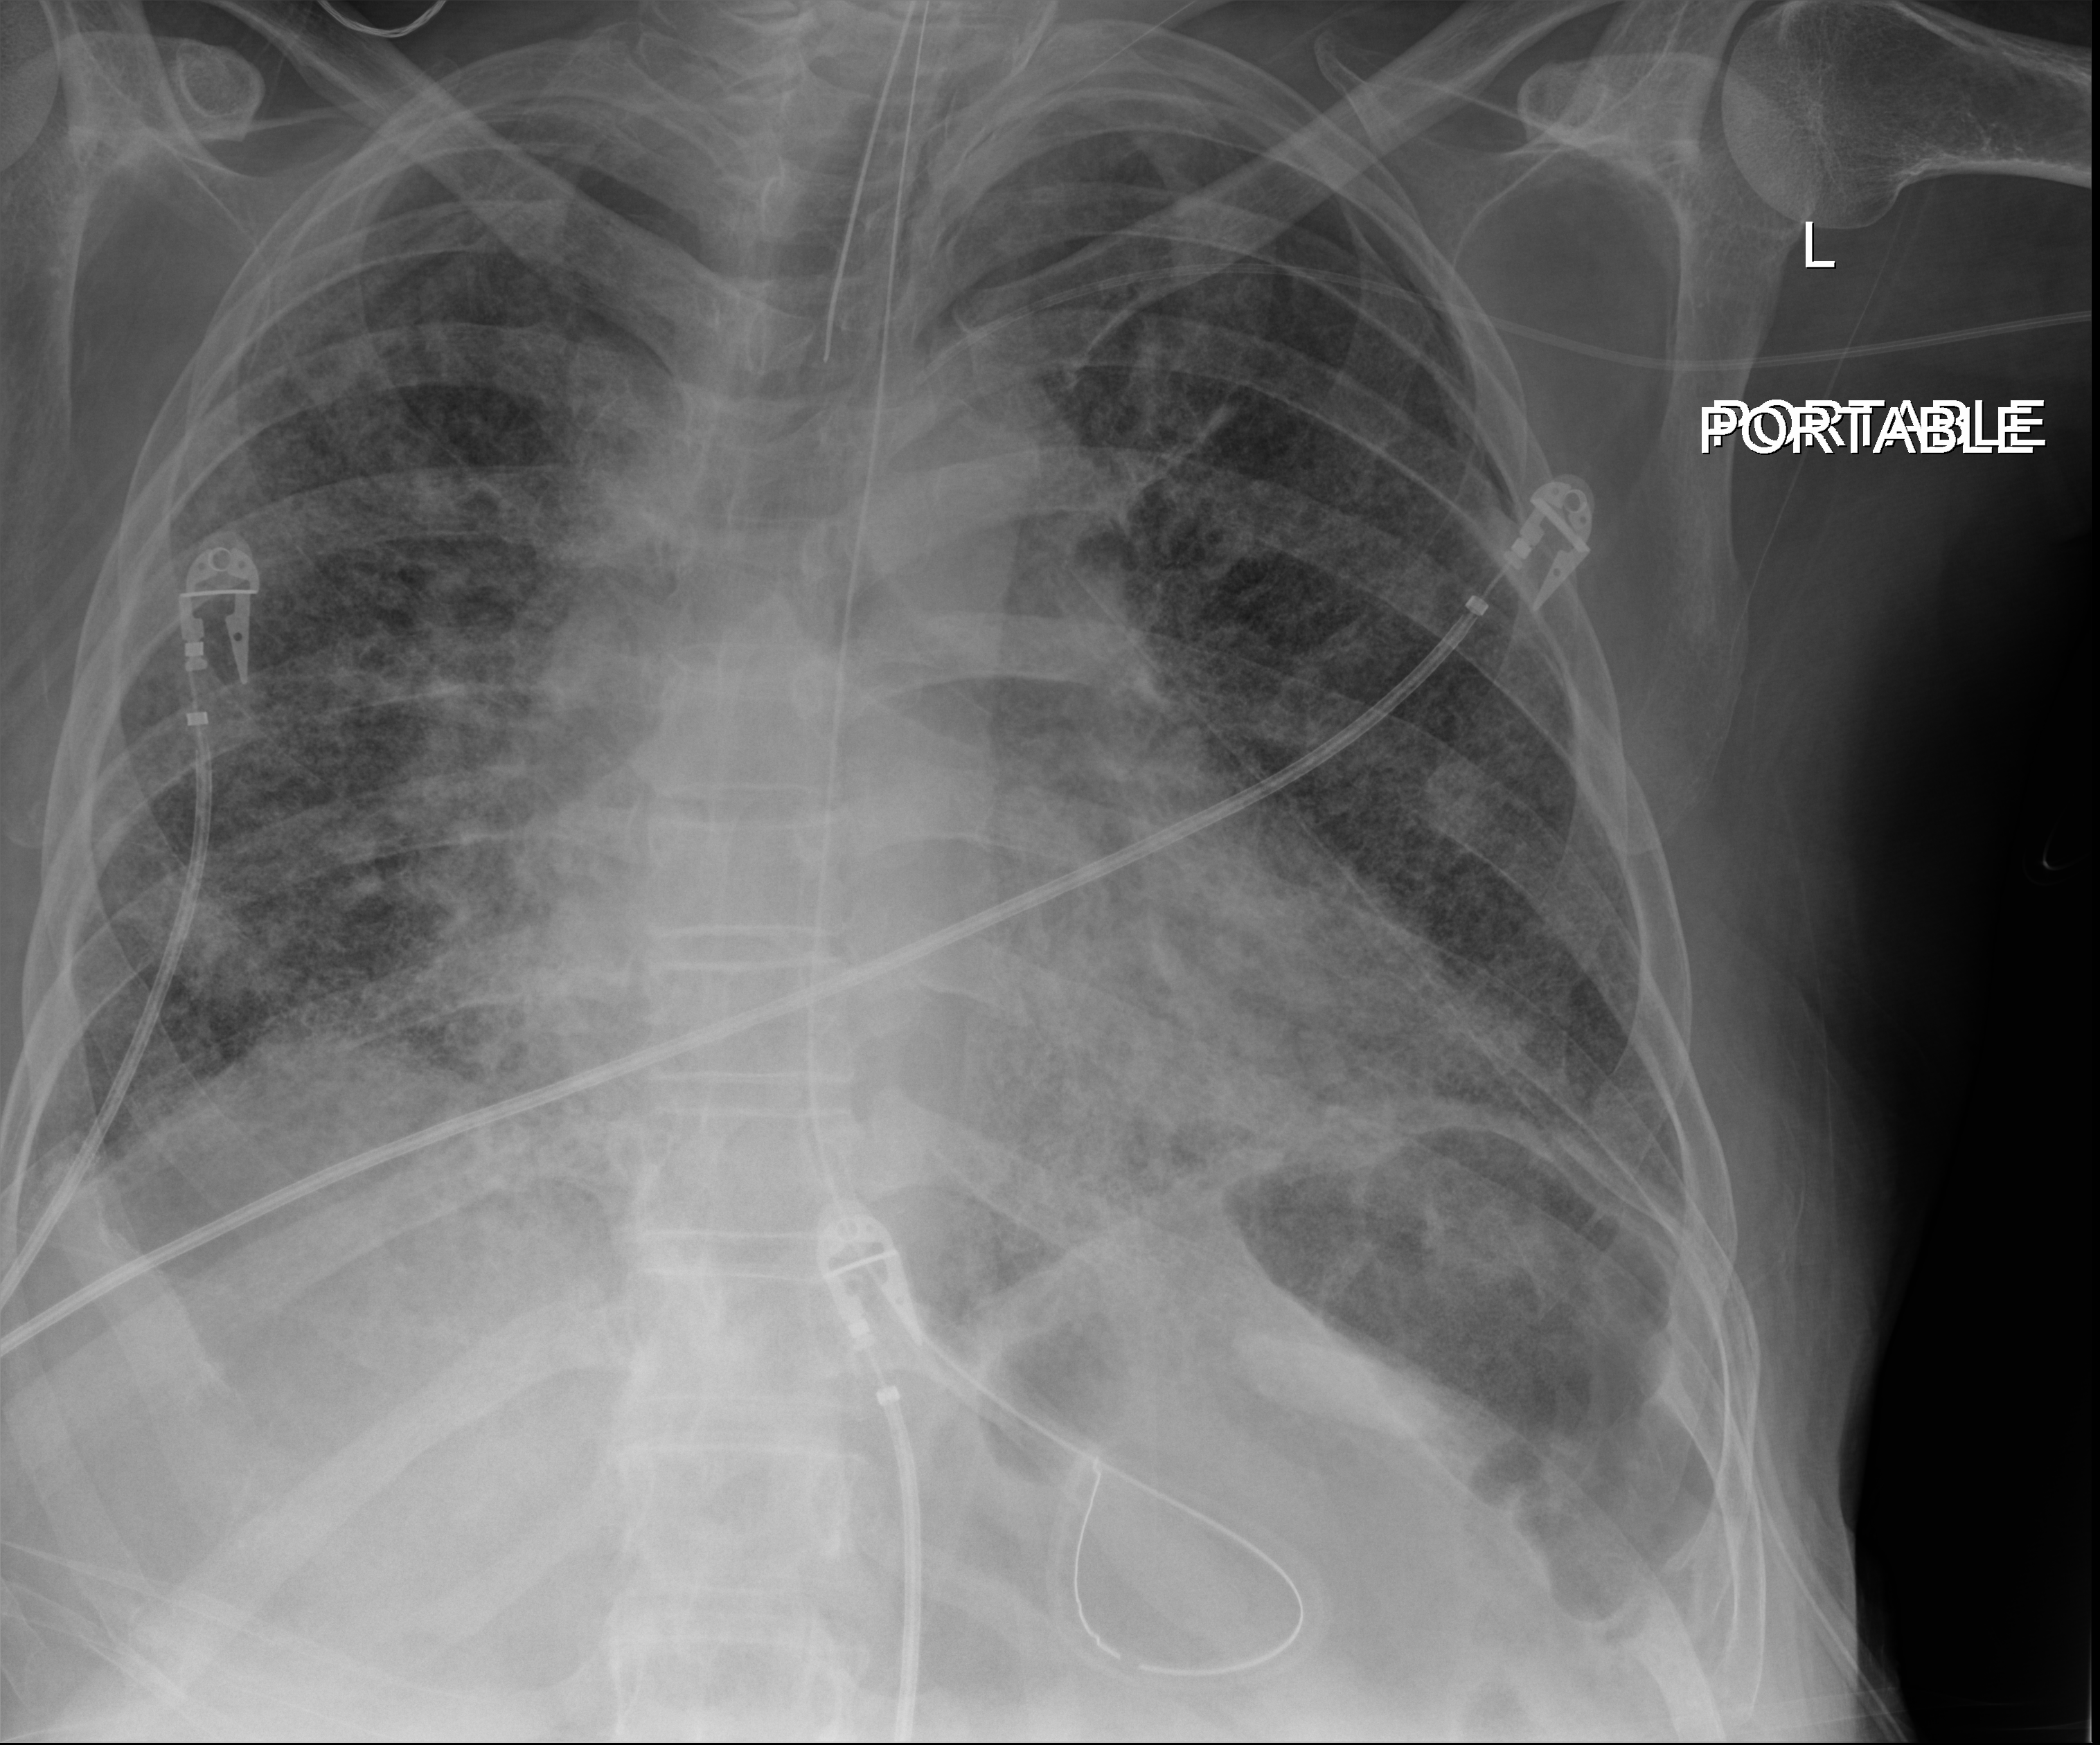
Portable chest radiograph; posteroanterior (PA) projection. Patient hospitalised with COVID-19; male, aged 60–74 years.
From the hospital-stay record, not from the radiograph (when in the stay this image was taken is not recorded): admitted to intensive care during this hospital stay: yes.